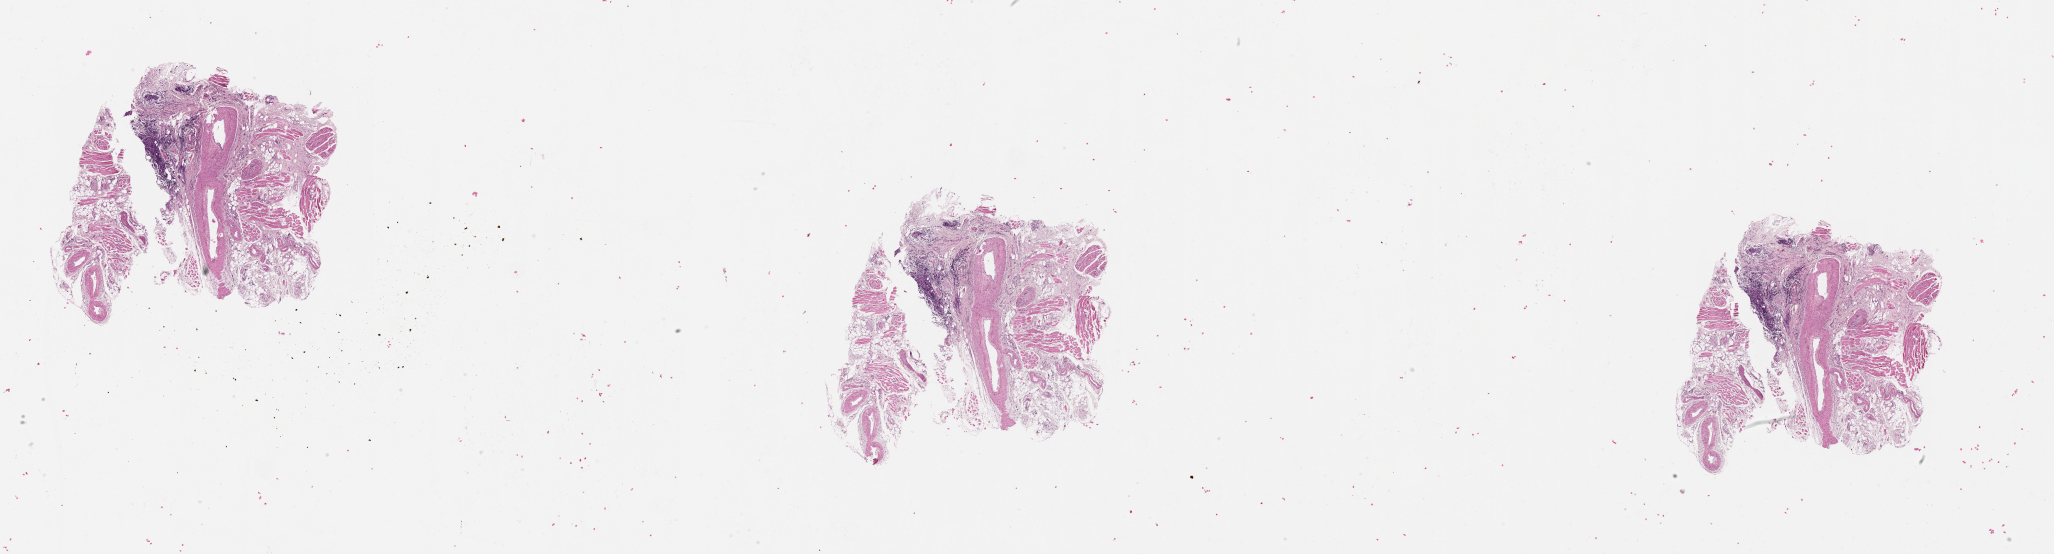
Whole-slide histology image, Hematoxylin and eosin (H&E) stained — whole scanned area (about 33.1 x 8.9 mm, slide scanned at 20x) shown as a low-resolution overview. Head and neck, tissue type not recorded. Male, 71 y/o.
* patient diagnosis: Squamous cell carcinoma, NOS (floor of mouth, NOS)